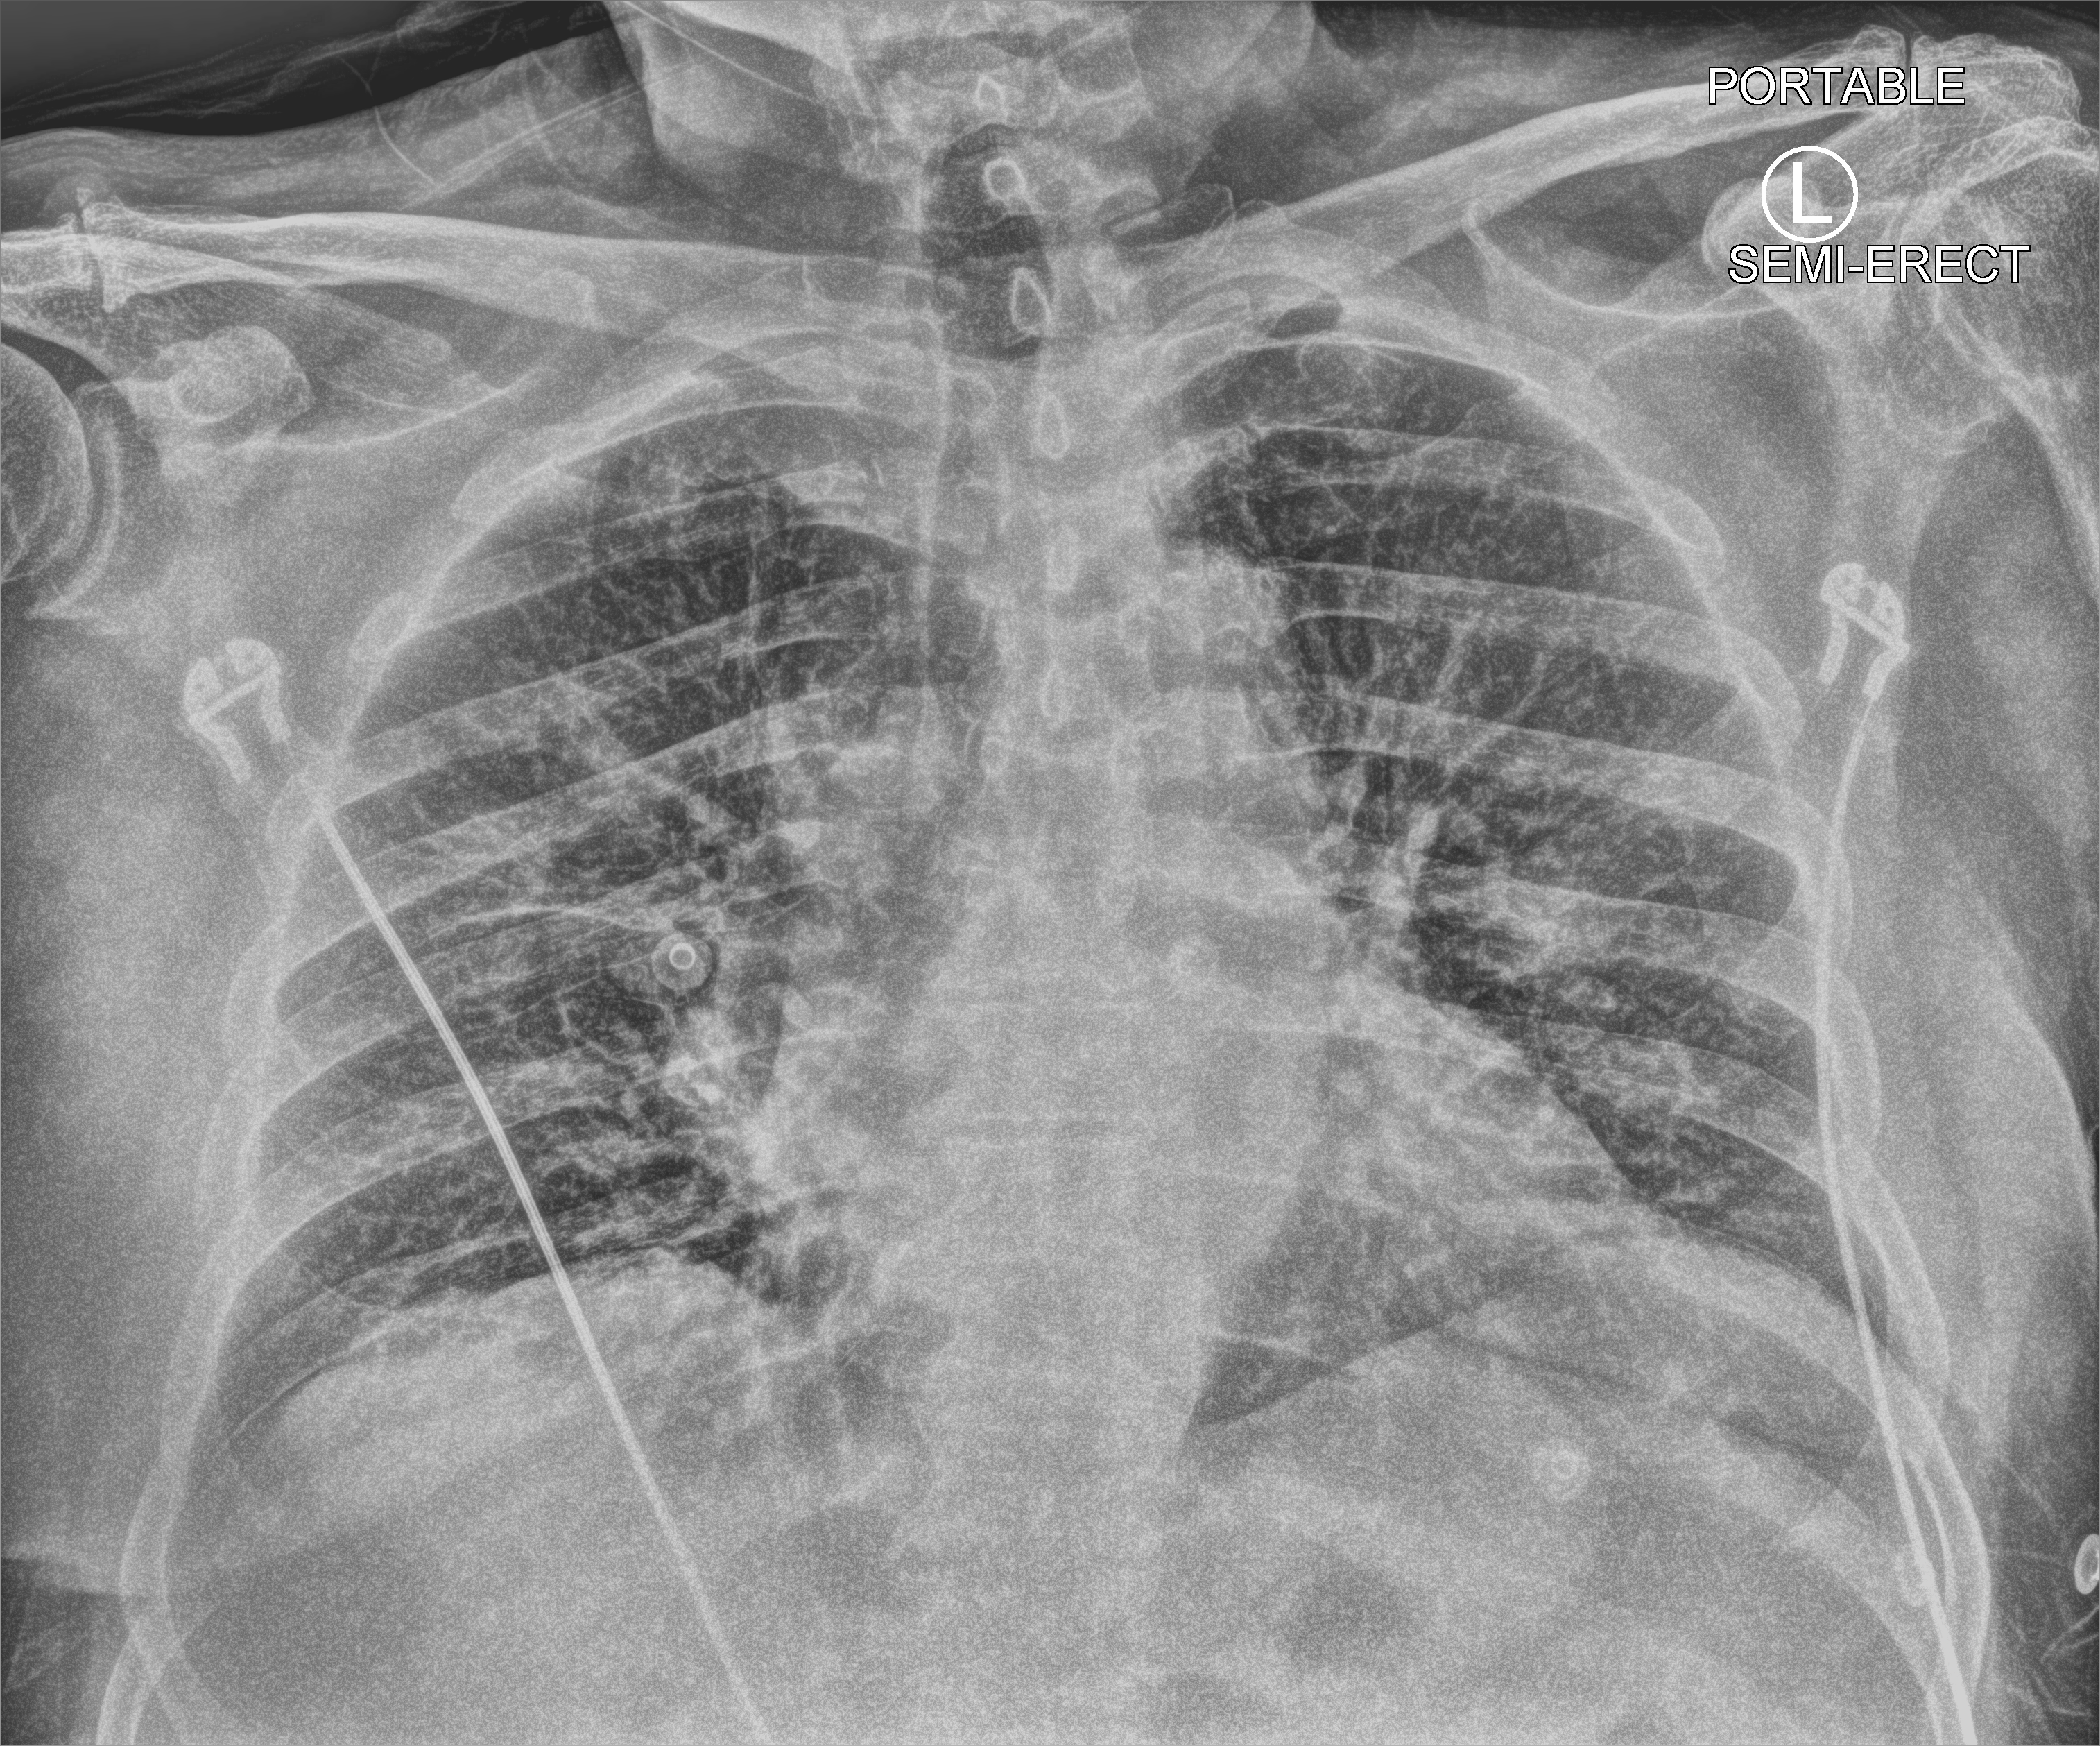
Chest X-ray (portable); anteroposterior (AP) projection. Male patient hospitalised with COVID-19, age 60–74 years.
From the hospital-stay record, not from the radiograph (when in the stay this image was taken is not recorded):
- mechanically ventilated during this hospital stay: no